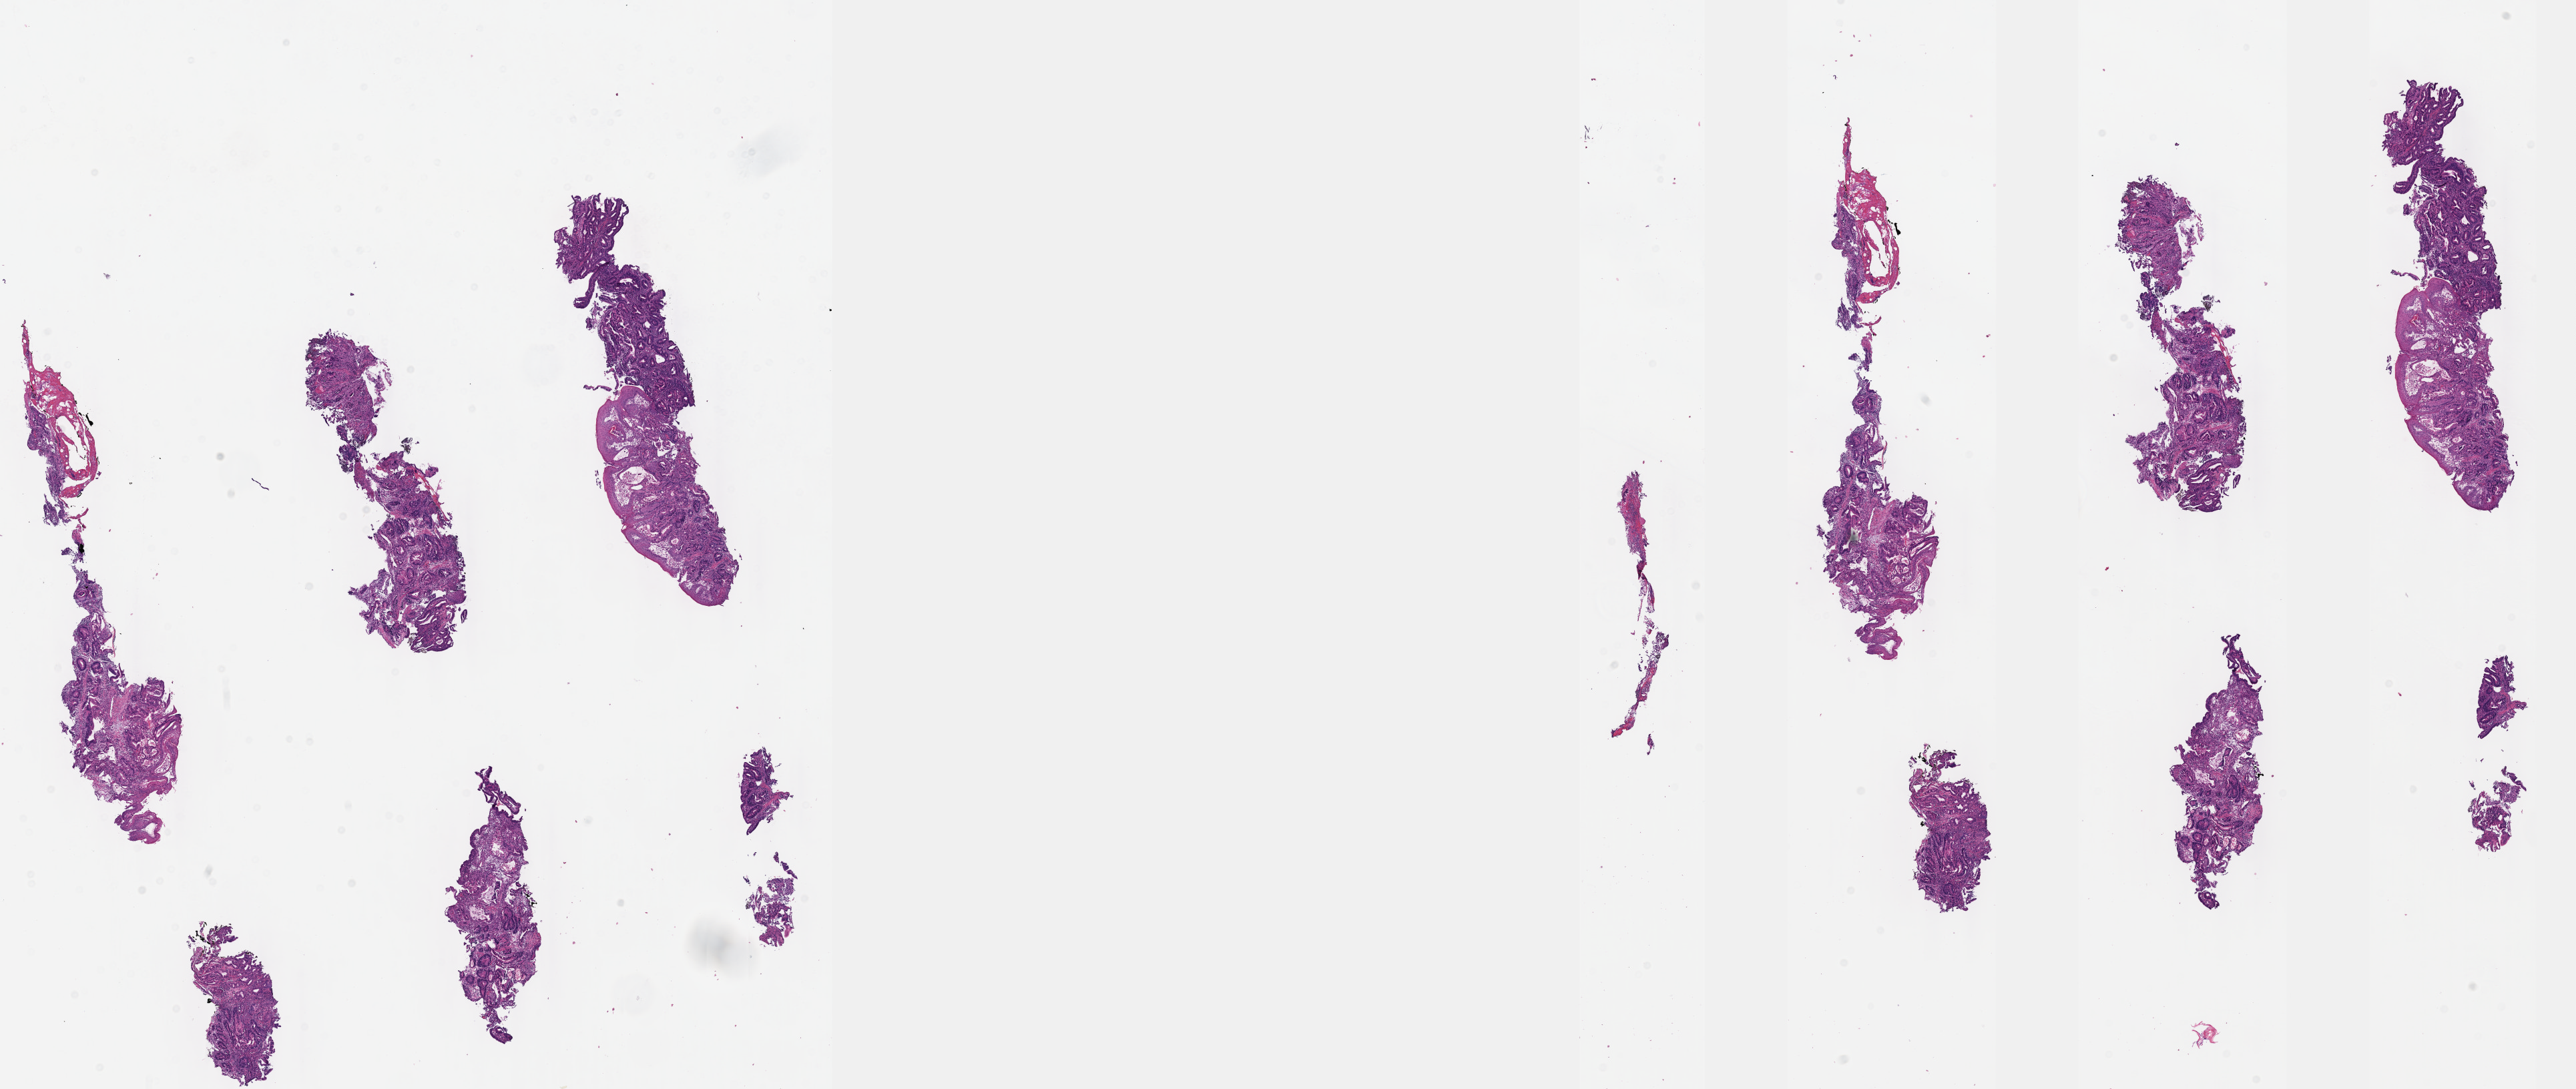
Digitized H&E-stained tissue section (whole slide) — a low-resolution overview of the entire scanned area, about 31.2 x 13.2 mm (slide scanned at 40x); FFPE section; sample: primary tumour, esophagus. Male, age 74 years at initial diagnosis. Histologic grade: G2 (moderately differentiated).
• histologic diagnosis: Adenocarcinoma, NOS (lower third of esophagus)